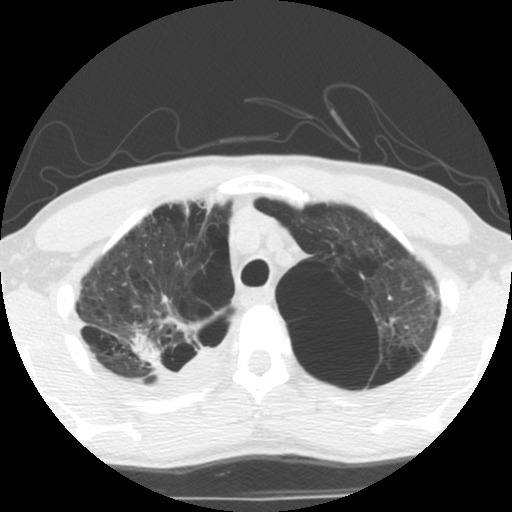
Low-dose screening chest CT, axial slice. Second annual screen. Lung window (W 1500 / L -600 HU). 2.5 mm slice thickness. 140 kVp. 512 × 512 image matrix, field of view 295 × 295 mm. Male participant, aged 62 years at enrolment. Current smoker at enrolment.
- Lesion marked by an expert reader, bounding box (x1, y1, x2, y2) in pixels: (122, 318, 210, 389).
- The exam's reader record, not a measurement of the box and not confirmed to be the same lesion: non-calcified nodule or mass ≥4 mm, 35 × 25 mm, soft tissue attenuation.
- Official screen result: positive, other.
- Participant outcome: lung cancer diagnosed 14 days after this screen — non-small cell carcinoma, right upper lobe, poorly differentiated (G3), stage IA (AJCC 6th edition), 70 mm at pathology.